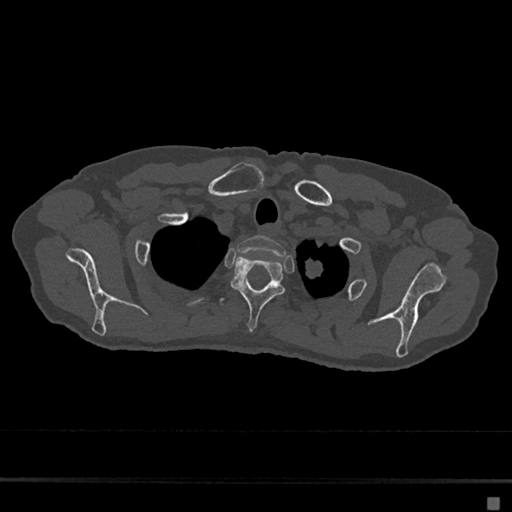
CT including the spine, one axial slice; slice 575 of 797 in the series (ordered by position); bone window (W 1800 / L 400 HU); 0.5 mm slice thickness; 512 × 512 image matrix, field of view 360 × 360 mm. Patient: female, 68 years. From the clinical record (not read from this slice): primary cancer: renal.
Structures marked on this image (semi-automatic segmentation, software-assisted and operator-edited):
- T1 vertebra: bounding box [x1, y1, x2, y2] px = [237, 235, 286, 256]
- T2 vertebra: [231, 255, 285, 331]
- T3 vertebra: [219, 298, 225, 303]